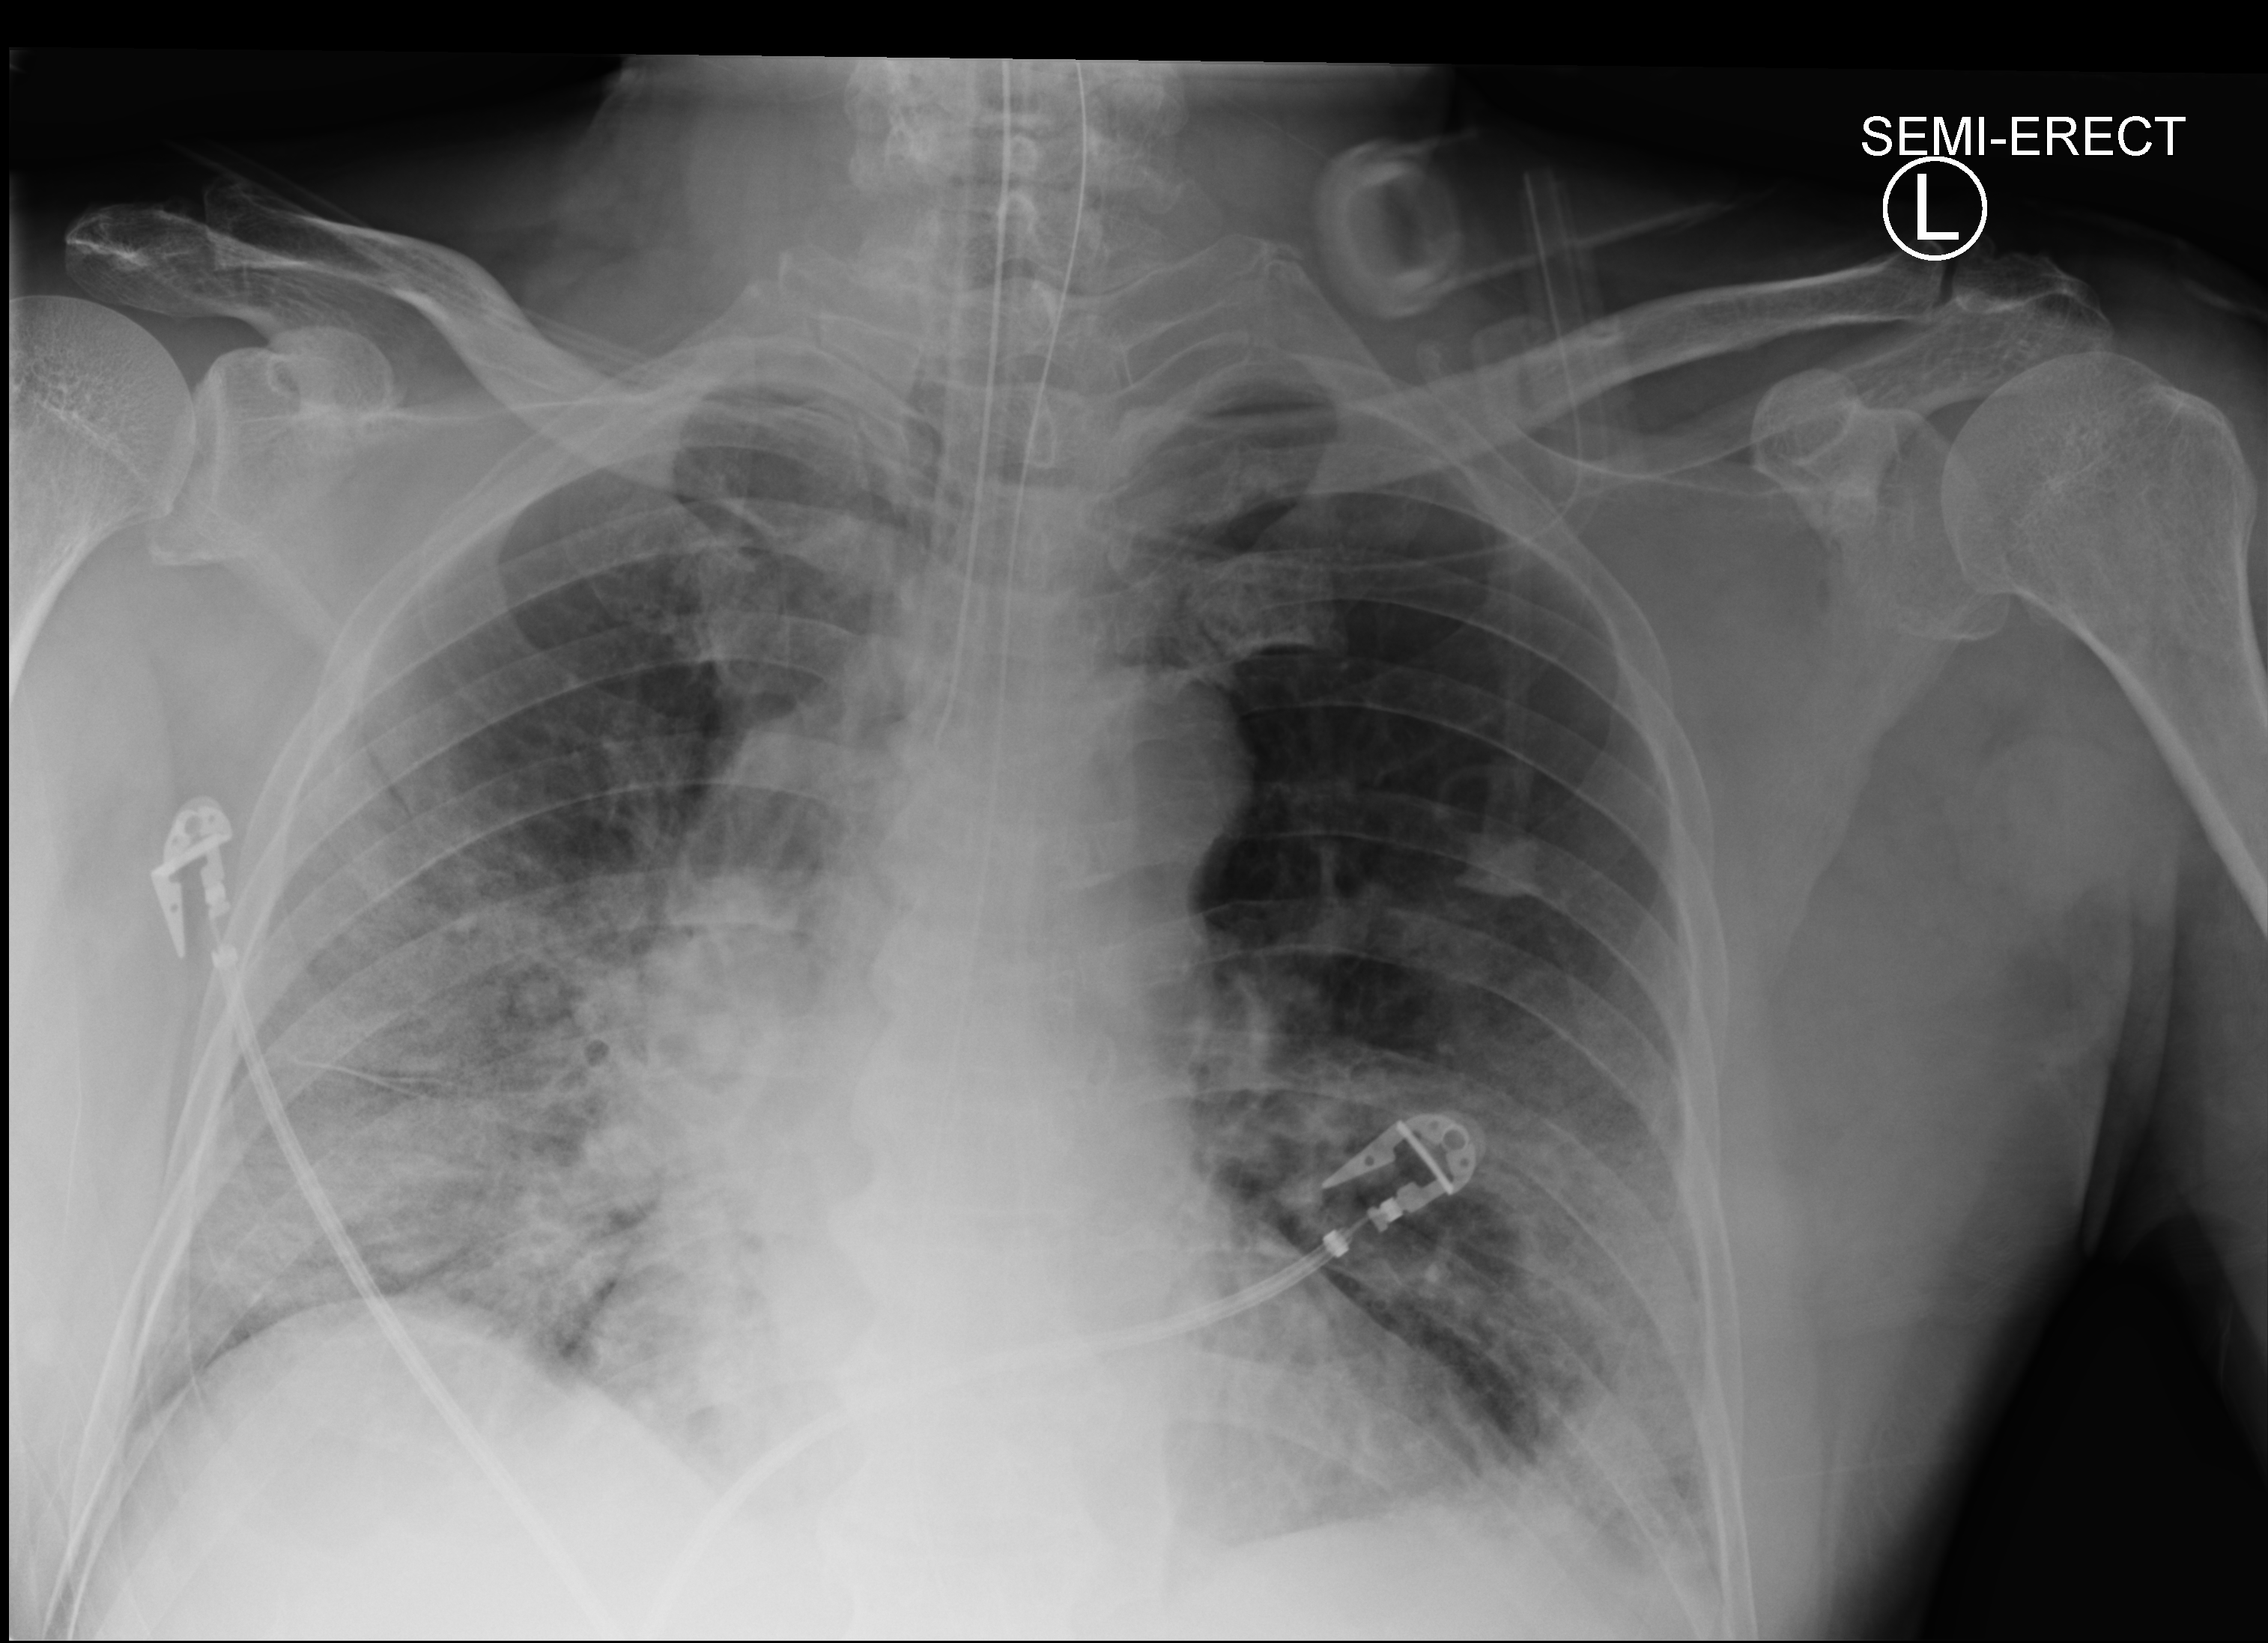
Bedside chest radiograph (computed radiography), anteroposterior (AP) projection. Male patient hospitalised with COVID-19, age 60–74 years.
From the hospital-stay record, not from the radiograph (when in the stay this image was taken is not recorded):
- other chronic lung disease (admission record): no
- length of hospital stay: 26 days